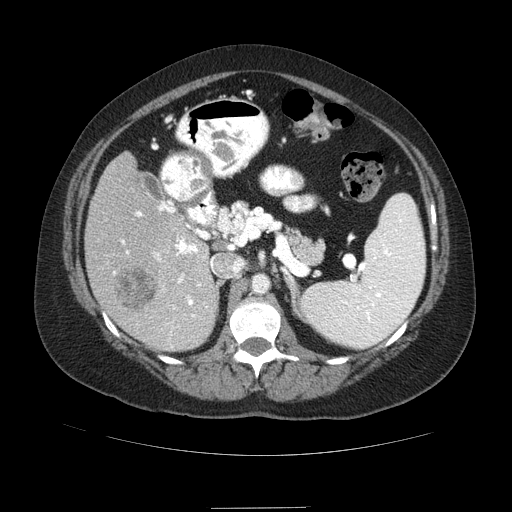
Contrast-enhanced abdominal CT (liver protocol), one axial slice; position 44 of 89 along the scan axis; reconstruction kernel STANDARD; 120 kVp; soft-tissue window (W 400 / L 40 HU); 2.5 mm slice thickness; 512 × 512 image matrix, field of view 400 × 400 mm. From the clinical record (not read from this slice): diagnosis: hepatocellular carcinoma (patient treated with transarterial chemoembolisation; whether this scan precedes or follows treatment is not stated here); TNM stage (as recorded): Stage-IIIB; Child-Pugh class: A.
Structures marked on this image (semi-automatically segmented with operator editing):
- liver parenchyma outside the tumour (the mass and vessels are separate outlines, so this box may not span the whole liver): bounding box [x1, y1, x2, y2] px = [84, 152, 218, 350]
- mass: [115, 266, 156, 313]
- liver vessels: [113, 206, 205, 347]